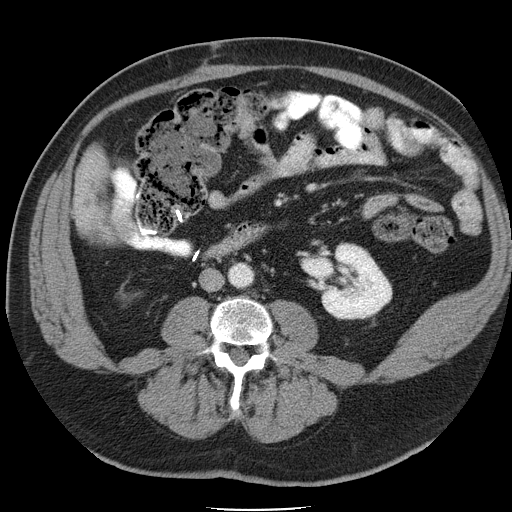
Contrast-enhanced abdominal CT, one axial slice. Position 9 of 45 along the scan axis. 120 kVp. Intravenous contrast given. Soft-tissue window (W 400 / L 40 HU). 5 mm slice thickness. 512 × 512 image matrix. Male patient, age 65 years. Case-level facts recorded for this patient, not image findings: diagnosis: colorectal cancer liver metastases, imaged before liver resection.
Structures marked on this image (outlined manually by an expert reader):
- liver: box from (x=79, y=156) to (x=104, y=220) px
- liver metastasis: (x=79, y=178)–(x=96, y=213)